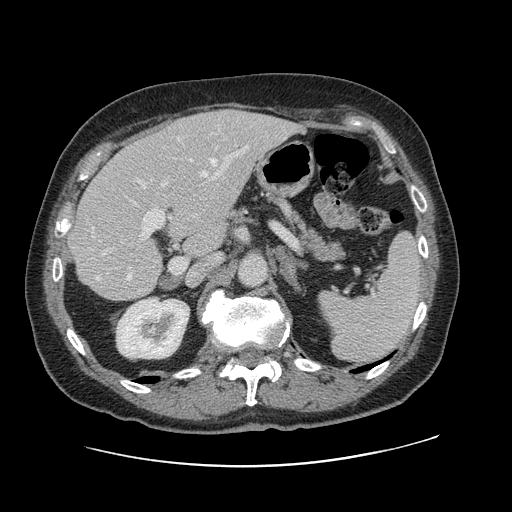
Contrast-enhanced abdominal CT, one axial slice; slice 67 of 138 in the series (ordered by position); 120 kVp; intravenous contrast given; soft-tissue window (W 400 / L 40 HU); 2.5 mm slice thickness; 512 × 512 image matrix, field of view 402 × 402 mm. Male patient, age 71 years. Case-level facts recorded for this patient, not image findings: diagnosis: colorectal cancer liver metastases, imaged before liver resection; multiple liver metastases: no; largest metastasis: 3.3 cm; disease in both lobes: no.
Outlined on this slice (manually delineated by an expert):
- hepatic veins: bounding box (x1, y1, x2, y2) in pixels: (92, 159, 223, 280)
- liver: (71, 110, 296, 300)
- planned liver remnant (the part of the liver to remain after resection): (71, 145, 222, 300)
- portal vein (with intrahepatic branches): (90, 145, 249, 274)